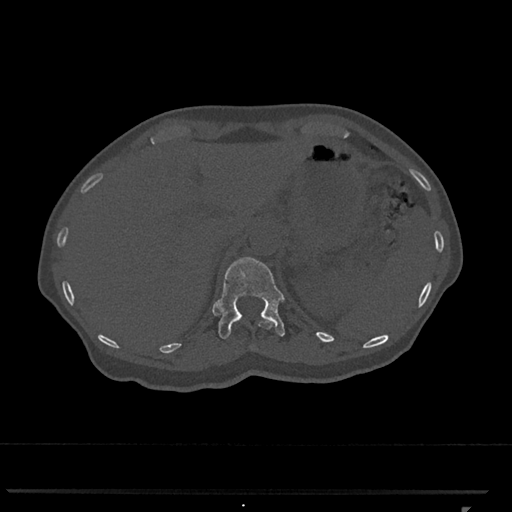
CT including the spine, one axial slice; slice 478 of 793 in the series (ordered by position); bone window (W 1800 / L 400 HU); 512 × 512 image matrix. Patient: female, 62 years. Case-level facts recorded for this patient, not image findings: primary cancer: renal.
Outlined on this slice (semi-automatic segmentation, software-assisted and operator-edited):
- T11 vertebra: bounding box <259,320,273,329> (left, top, right, bottom; pixels)
- T12 vertebra: <215,257,285,339>